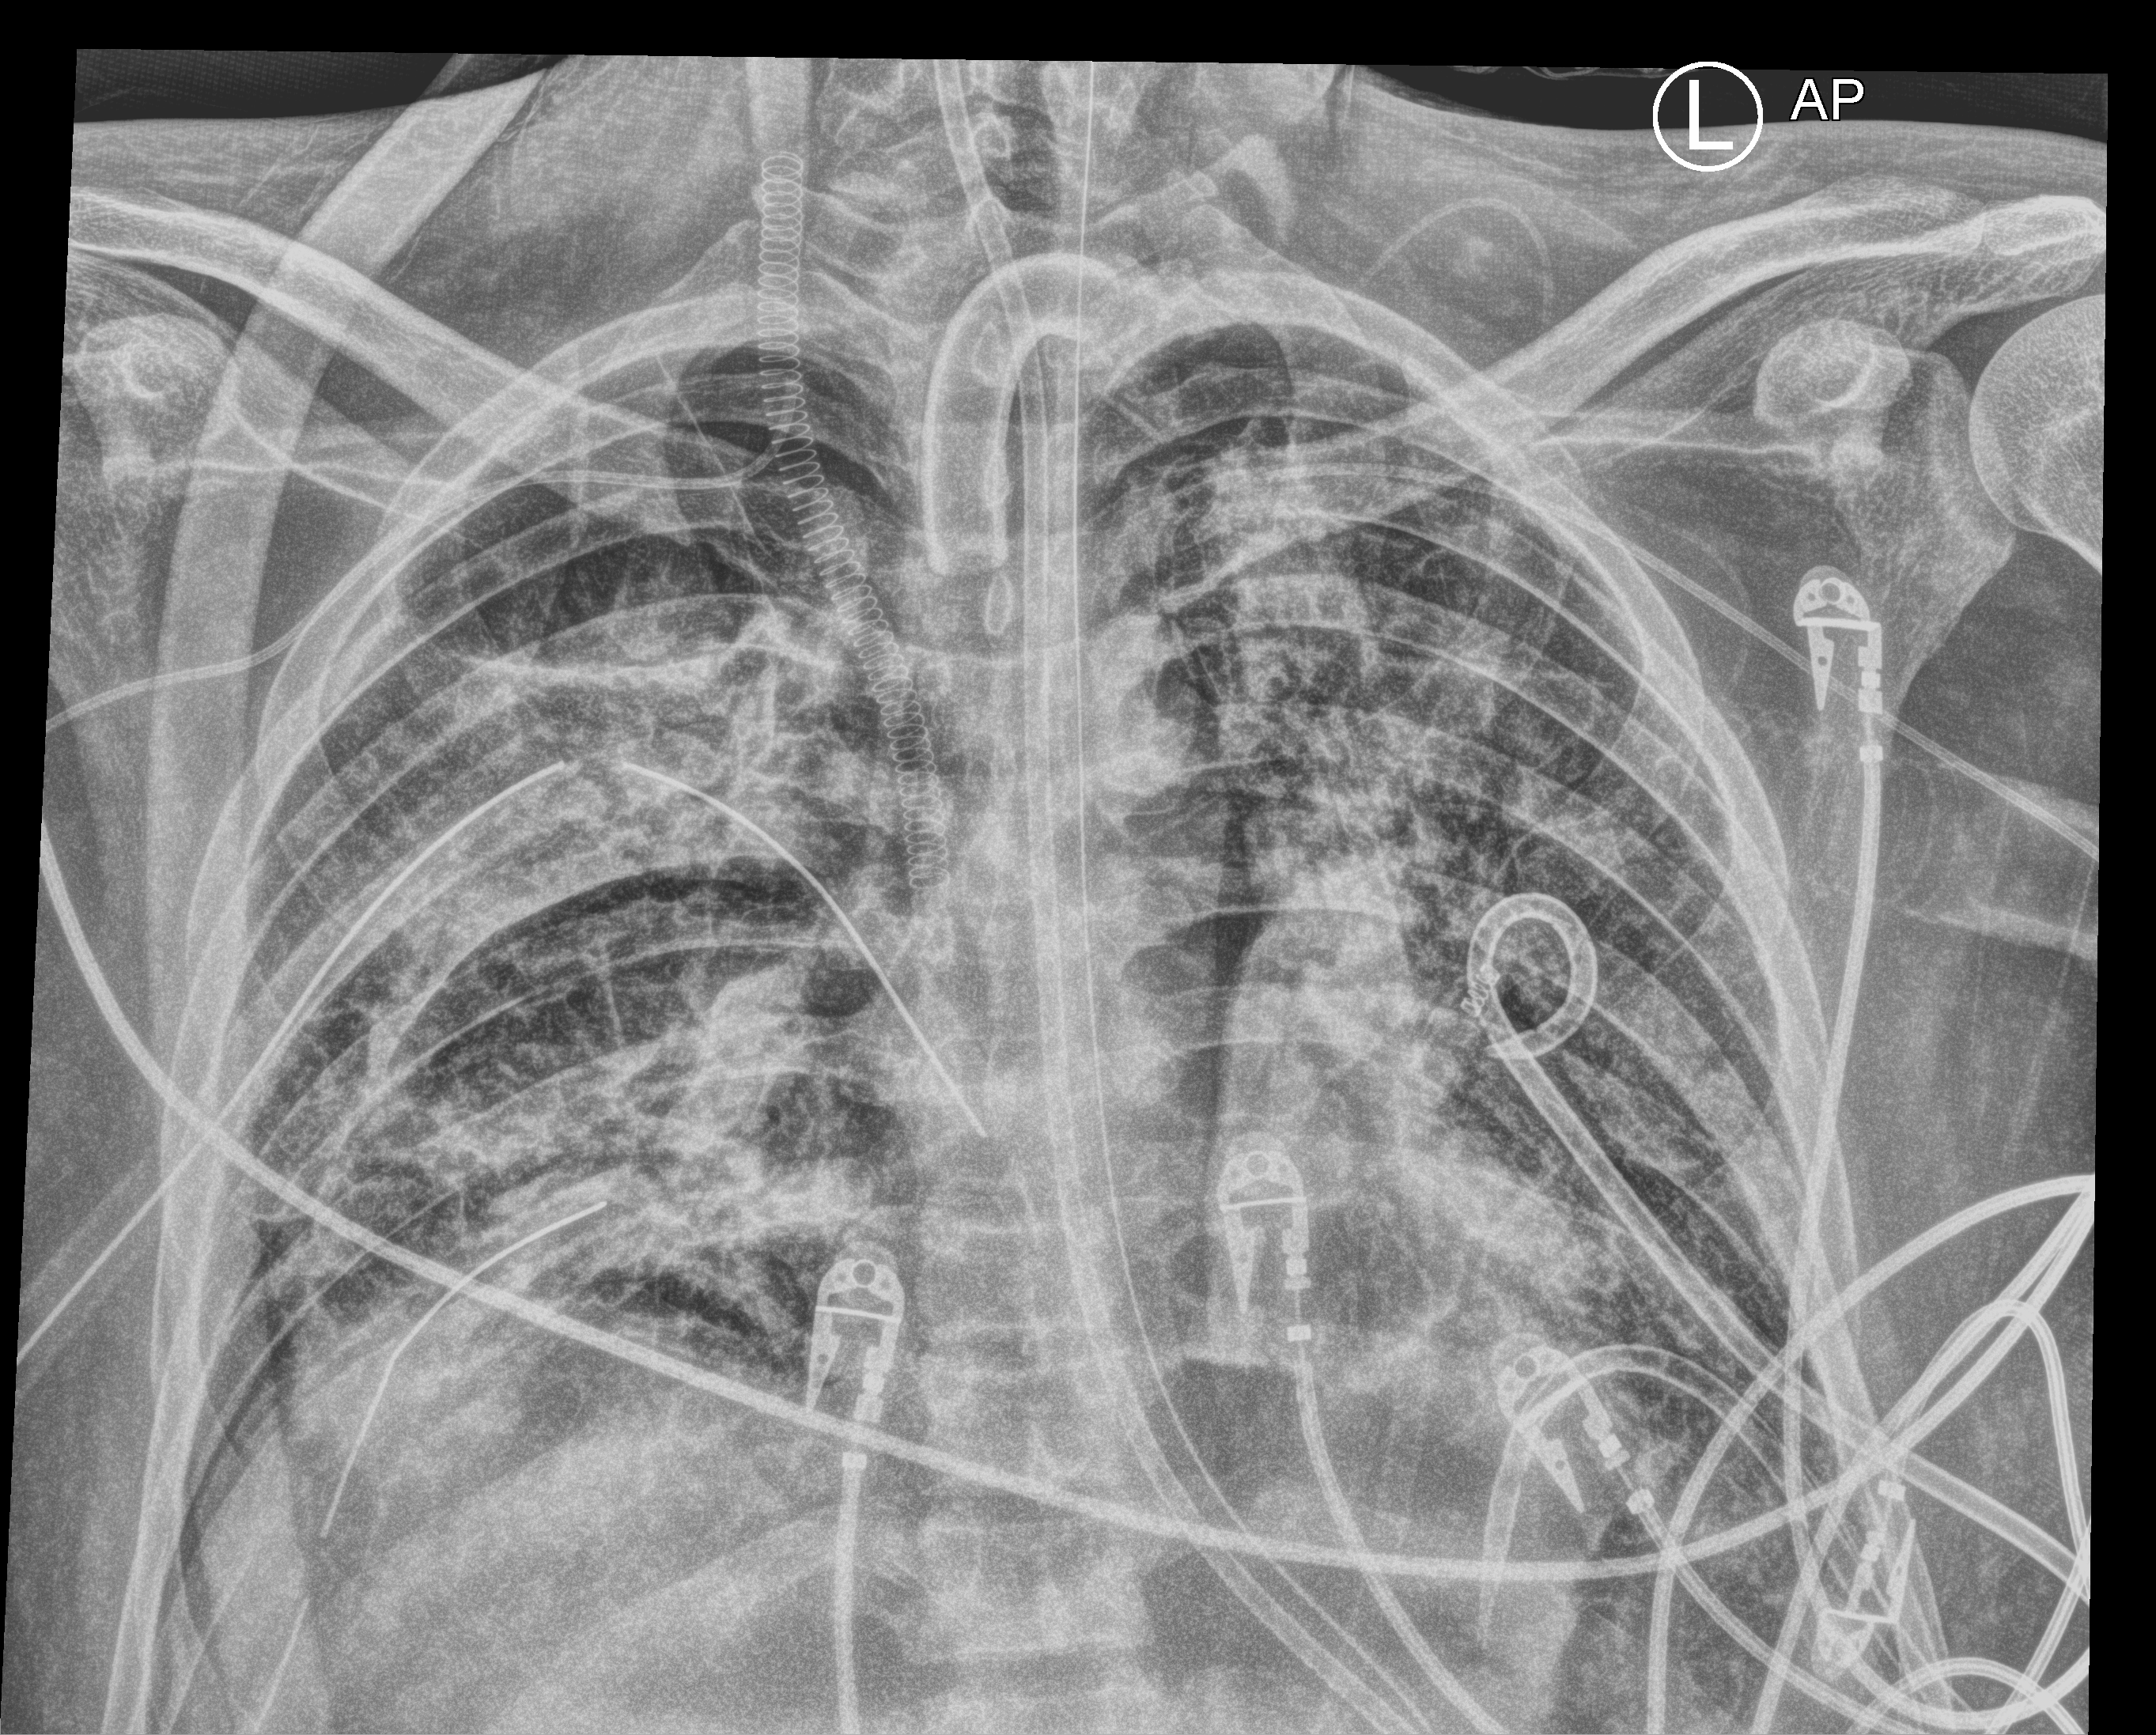
Portable chest radiograph; anteroposterior (AP) projection. Adult patient hospitalised with COVID-19, age 18–59 years.
From the hospital-stay record, not from the radiograph (when in the stay this image was taken is not recorded):
- hypertension (admission record): no